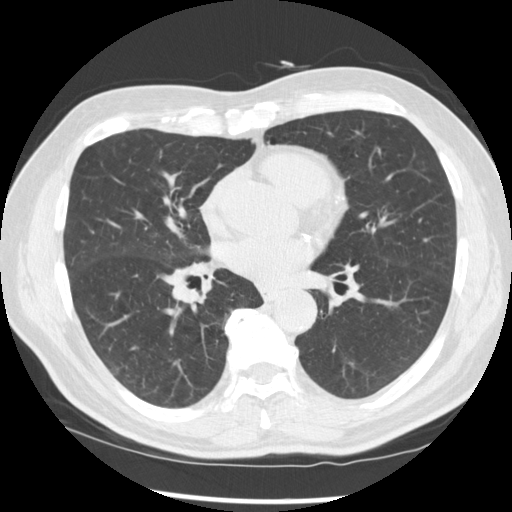
Low-dose screening chest CT, one axial slice; slice 136 of 277 in the series (ordered by position); reconstruction kernel STANDARD; 120 kVp; lung window (W 1500 / L -600 HU); 2.5 mm slice thickness; 512 × 512 image matrix.
Structures marked on this image (expert manual segmentation):
- lesion 1 (tumor, middle lobe of right lung): bounding box [x1, y1, x2, y2] px = [172, 283, 203, 304]